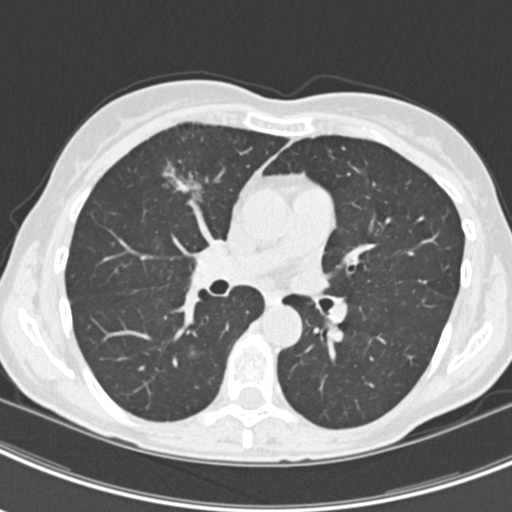
Chest CT (low-dose screening protocol), one axial image. Second screening round (one year after baseline). Lung window (W 1500 / L -600 HU). 2 mm slice thickness. Slice 88 of 219 in the series. 512 × 512 image matrix, field of view 298 × 298 mm. Female participant, aged 63 years at enrolment. Current smoker at enrolment.
Expert reader's lesion annotation, bounding box (x1, y1, x2, y2) in pixels: (160, 154, 220, 206). The screening reader recorded 9 non-calcified nodules or masses ≥4 mm on this exam (left upper lobe, right upper lobe, left upper lobe, left lower lobe, right middle lobe, left lower lobe, left lower lobe, right lower lobe, right lower lobe); which of them this box marks is not recorded. Official screen result: positive, other. Later outcome: lung cancer diagnosed 408 days after this screen (after the third annual screen) — bronchiolo-alveolar adenocarcinoma, NOS, right upper lobe, right middle lobe, right lower lobe, left upper lobe, left lower lobe, moderately differentiated (G2), stage IV (AJCC 6th edition).